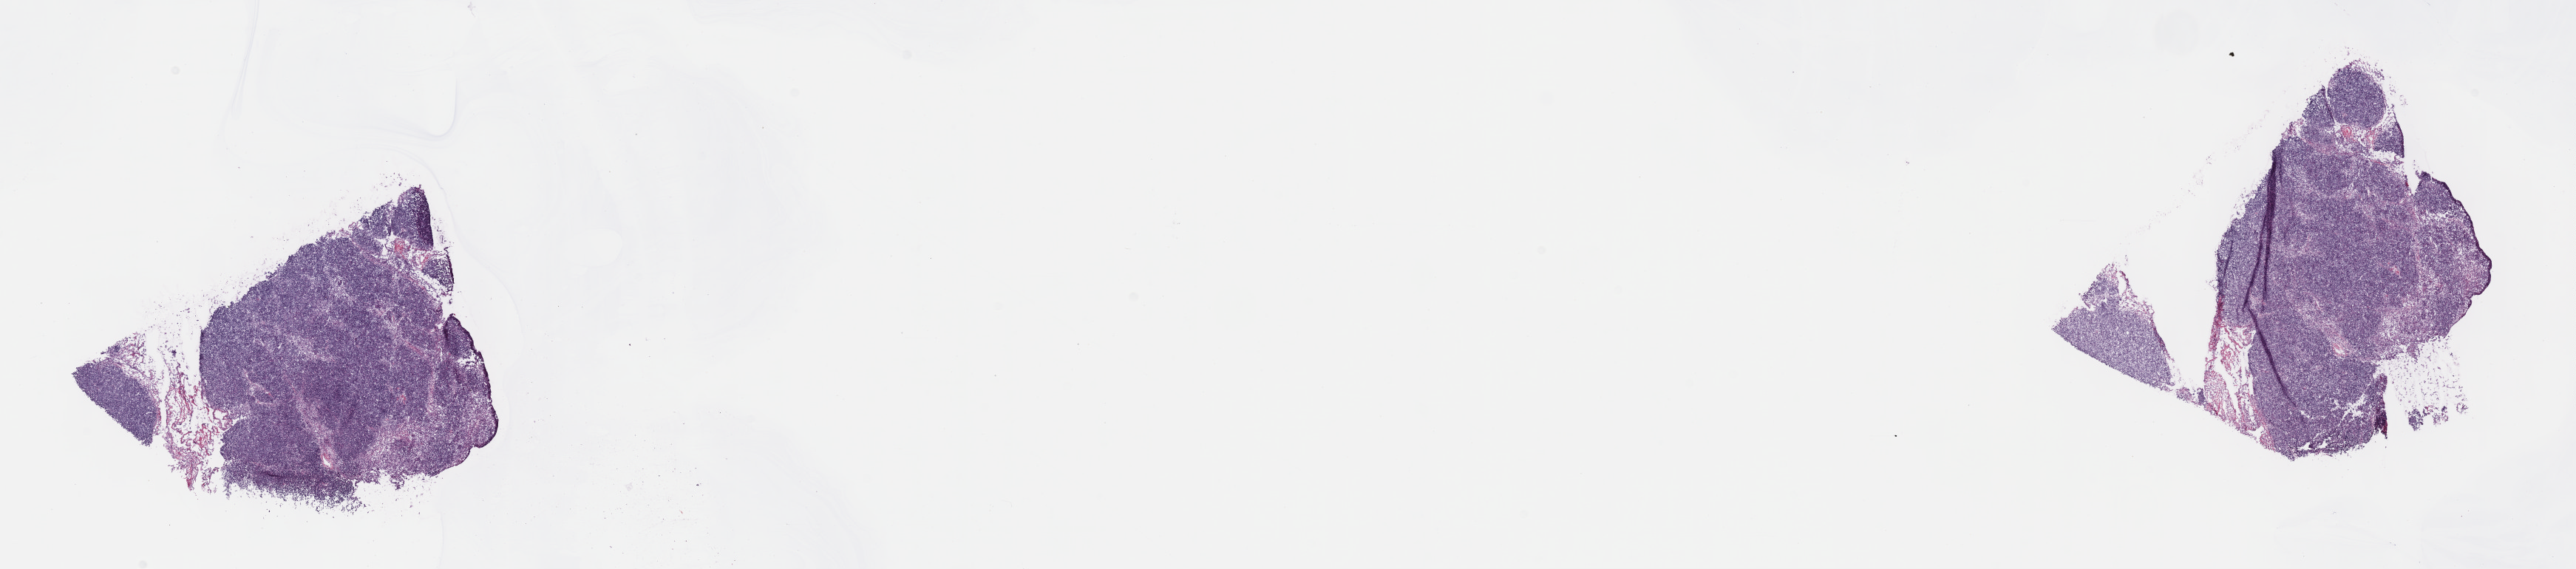
H&E whole-slide image, shown as a low-resolution overview of the whole scanned area (about 28.2 x 6.2 mm). Frozen section. Primary tumour sample from the thymus. Male patient; age at initial diagnosis 39 years. Pathologist review of this section (percent, as recorded): tumour cells 85%, tumour nuclei 85%, normal cells 0%, stromal cells 15%, necrosis 0%. Infiltration values recorded for this section: lymphocyte infiltration 2%, monocyte infiltration 1%, neutrophil infiltration 1%.
Histologic diagnosis: Thymoma, type AB, malignant.